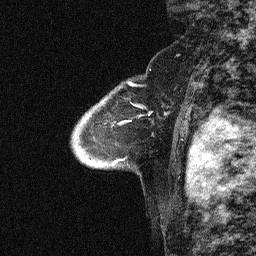
Breast MRI (dynamic contrast-enhanced), one sagittal slice; dynamic contrast-enhanced study with each time point stored as its own series, time point 2 of 3 at this slice position (early post-contrast, ordered by acquisition time); 1.5 T; TE 4.5 ms, TR 11 ms; 2.06 mm slice thickness; 256 × 256 image matrix, field of view 200 × 200 mm. Female patient, age 46 years. From the clinical record (not read from this slice): setting: breast cancer imaged before/during neoadjuvant chemotherapy; receptor status: HER2-positive.
Structures marked on this image (semi-automatically segmented with operator editing):
- analysis volume of interest (the breast-tissue region the enhancement analysis was run in; not a lesion): bounding box (x1, y1, x2, y2) in pixels: (46, 51, 180, 169)
- tumour enhancement mask (voxels above the 90 % enhancement threshold inside the analysis volume of interest): (117, 104, 150, 124)